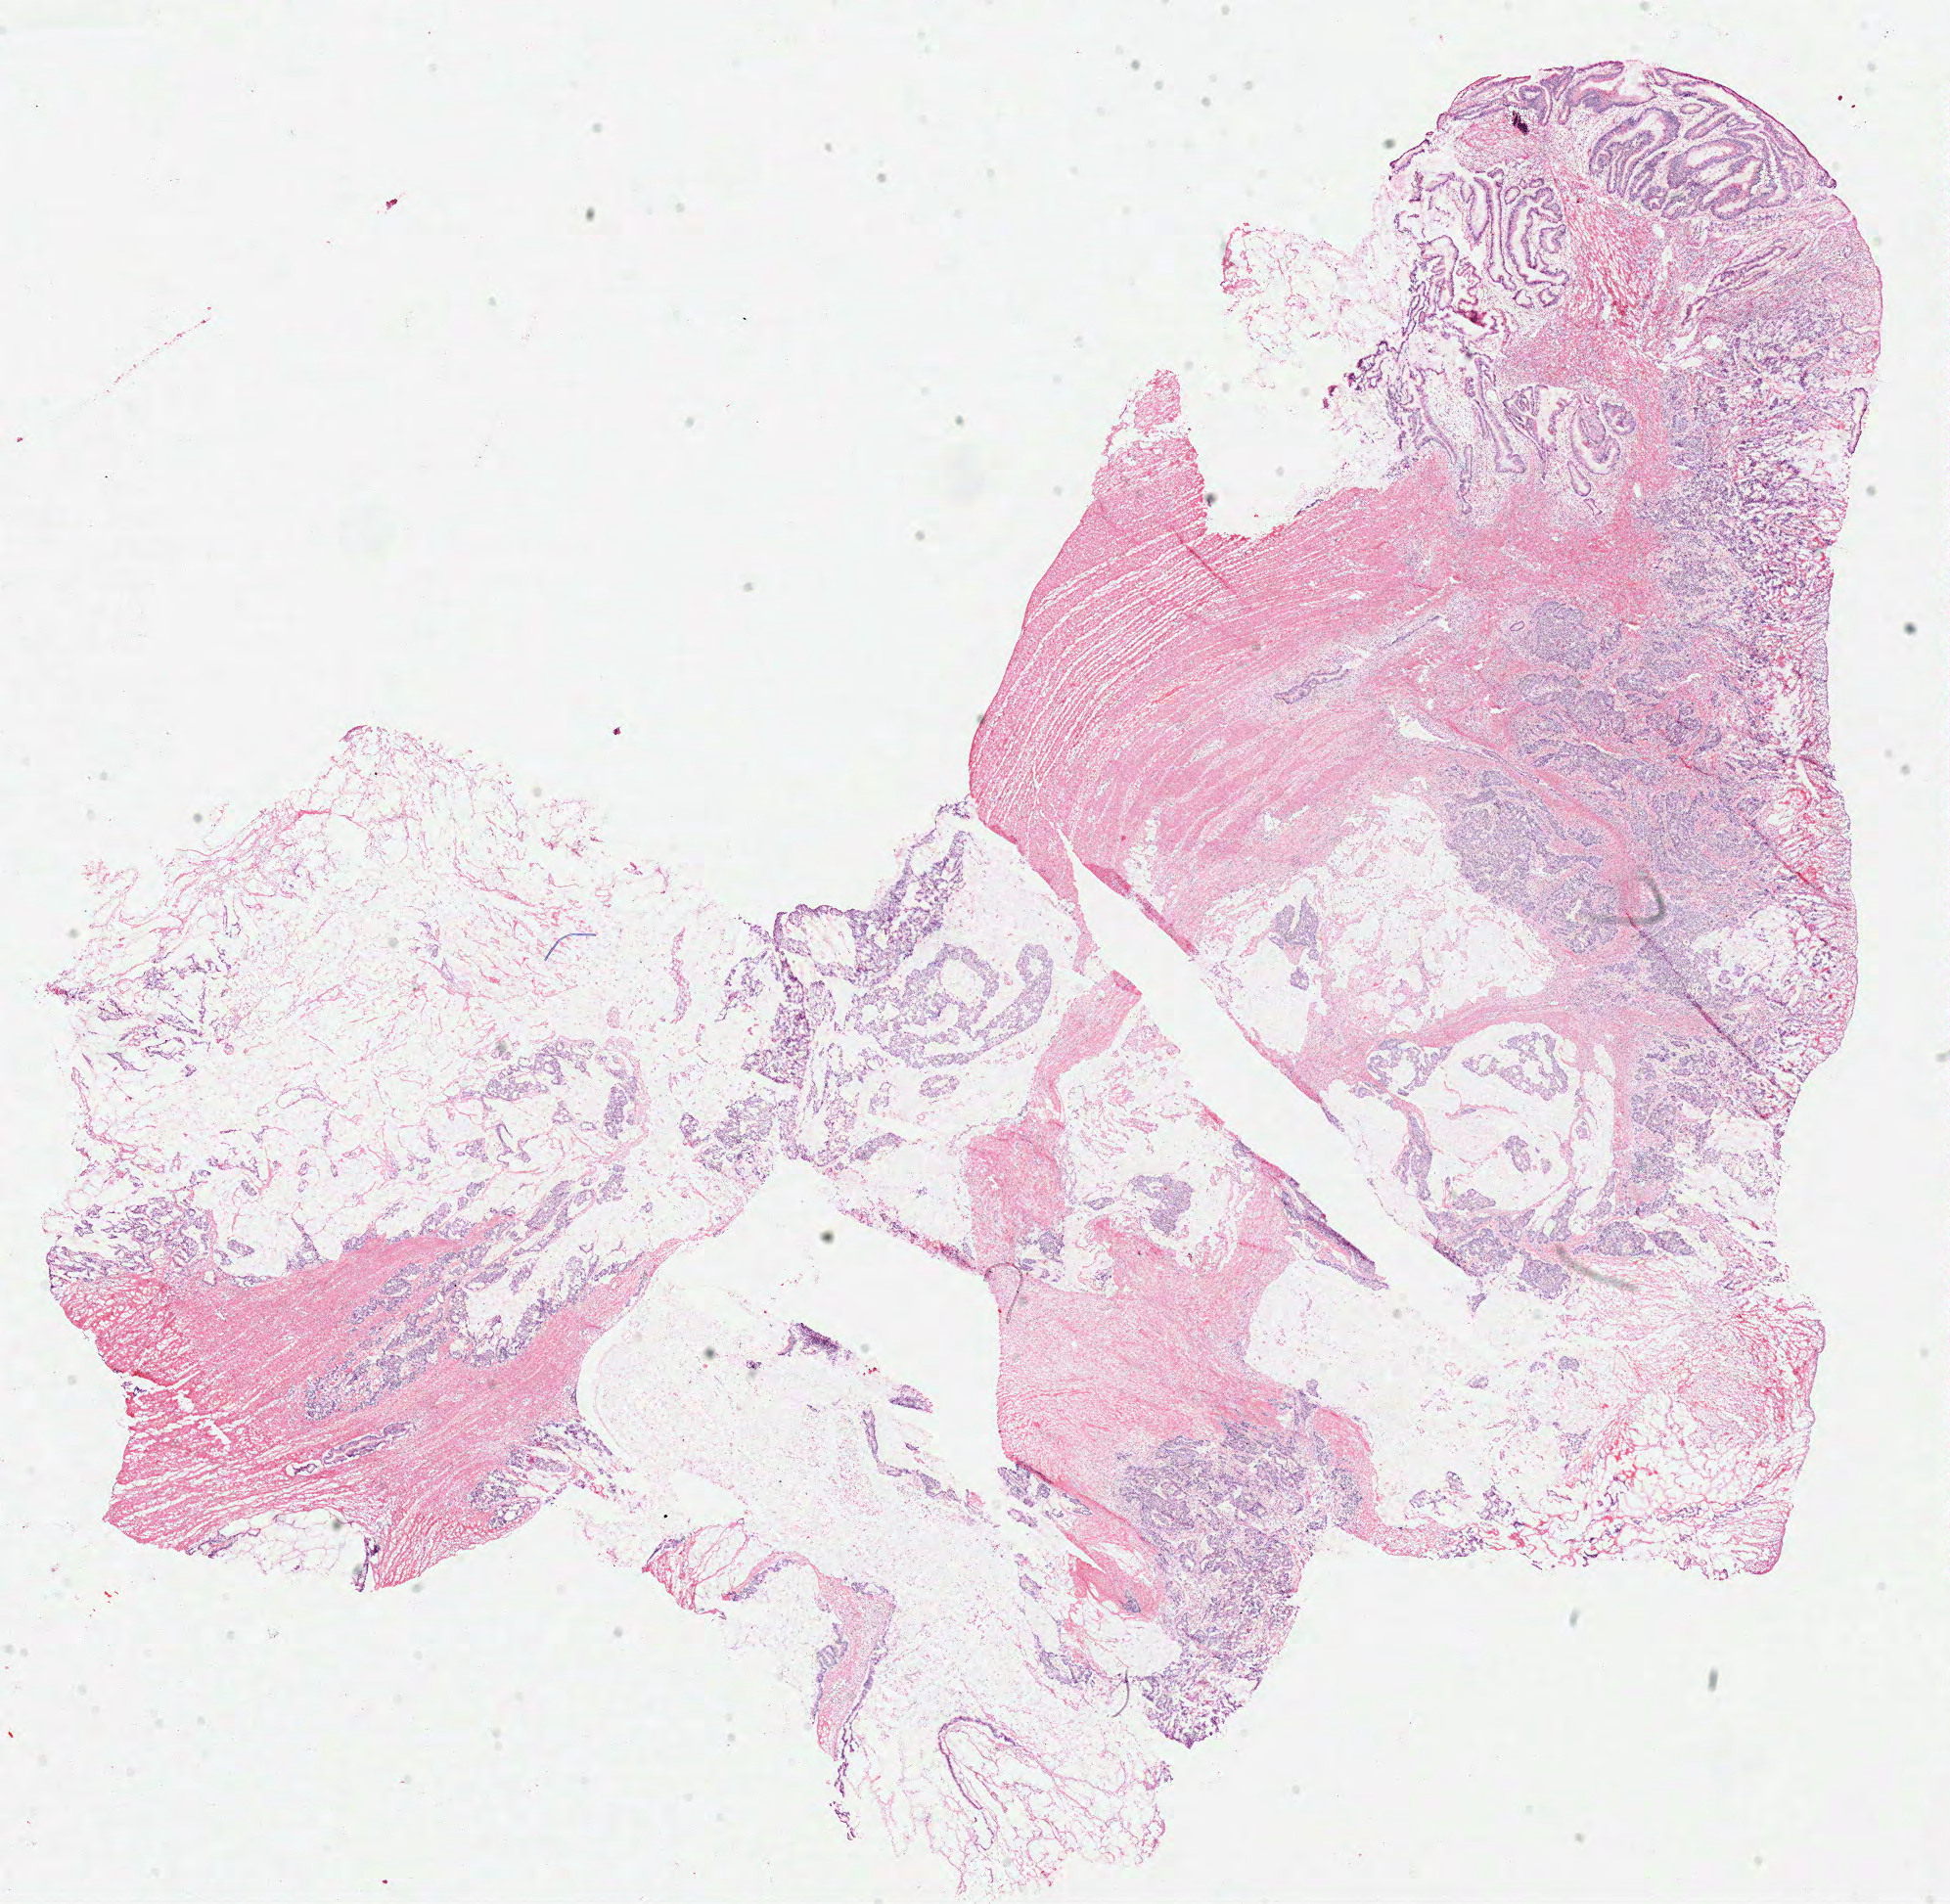
Digitized H&E tissue section (whole slide), low-resolution overview of the scanned area, about 15.7 x 15.3 mm (acquisition: 40x scan), frozen section, colon, primary tumour sample. Patient: male, age at initial diagnosis 60 years. Slide review estimates, as recorded: tumour cells 72%, tumour nuclei 85%, normal cells 8%, stromal cells 20%, necrosis 0%.
Lymph nodes positive (case pathology): 13 of 18 examined. AJCC pathologic stage: IIIC. Pathologic diagnosis: Mucinous adenocarcinoma.